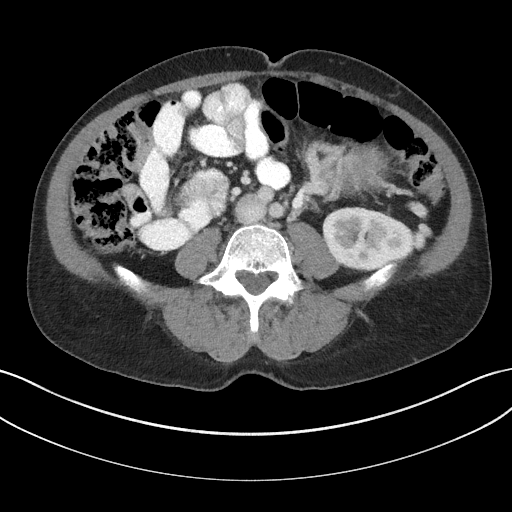
Contrast-enhanced abdominal CT, one axial slice; slice 73 of 147 in the series (ordered by position); reconstruction kernel I31f/3; 100 kVp; intravenous contrast given; soft-tissue window (W 400 / L 40 HU); 3 mm slice thickness; 512 × 512 image matrix, field of view 384 × 384 mm. Patient: male, 58 years. From the clinical record (not read from this slice): diagnosis: adrenocortical carcinoma; tumour side: left adrenal; tumour size at pathology: 22 cm; Ki-67 index: 26 %; stage (as recorded): 2.
Outlined on this slice (semi-automatically segmented with operator editing):
- mass: bounding box (x1, y1, x2, y2) in pixels: (345, 148, 391, 183)